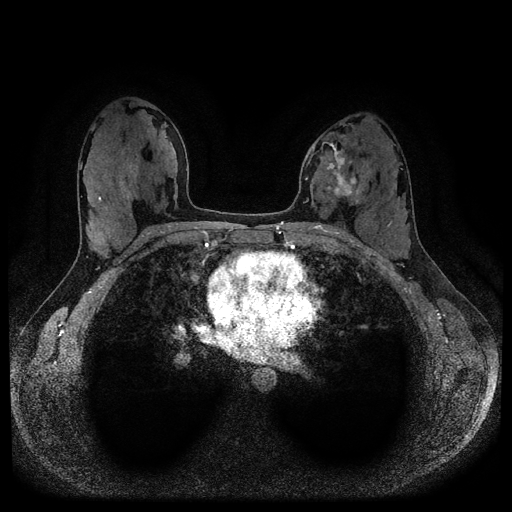
Breast MRI (dynamic contrast-enhanced, multi-phase), one axial slice; slice 55 of 116 in the series (ordered by position); dynamic contrast-enhanced series, time point 2 of 5 at this slice position (early post-contrast); 1.5 T; TE 2.6 ms, TR 5.3 ms; 512 × 512 image matrix, field of view 350 × 350 mm. Female patient, age 33 years.
Outlined on this slice (semi-automatically segmented with operator editing):
- breast lesion (labelled 'tumour' in the annotation; benign lesions carry a separate 'benign' label): box from (x=324, y=148) to (x=359, y=199) px